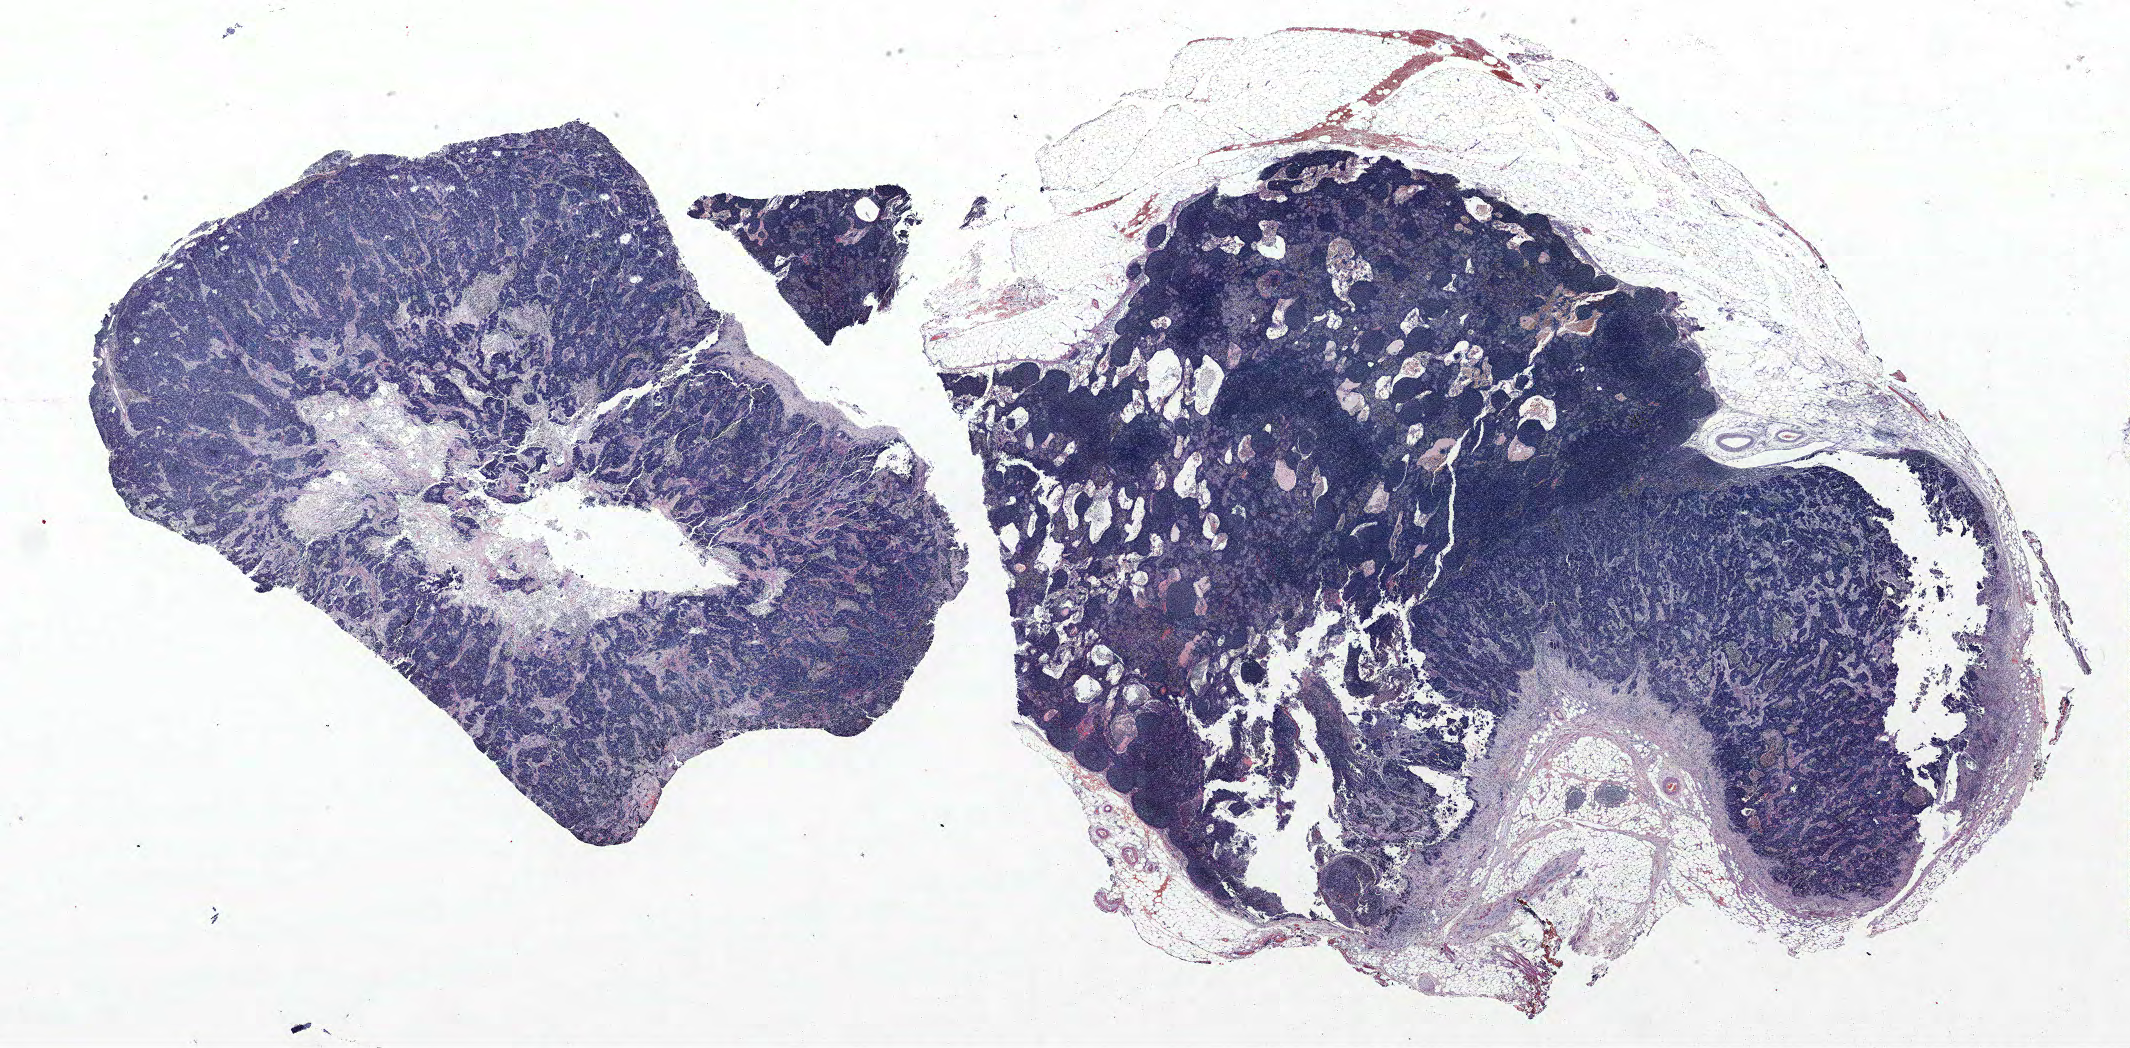
Whole-slide histology image, H&E-stained — low-resolution overview of the scanned area, about 34.1 x 16.8 mm. Formalin-fixed paraffin-embedded (FFPE) section. Lung tissue. Male patient, aged 64 at enrolment. Grade: poorly differentiated (G3).
* stage (AJCC 6th edition): IIIA
* participant's lung-cancer diagnosis: Neuroendocrine carcinoma, NOS
* primary tumour location (clinical record): left upper lobe
* tumour size (pathology): 11 mm